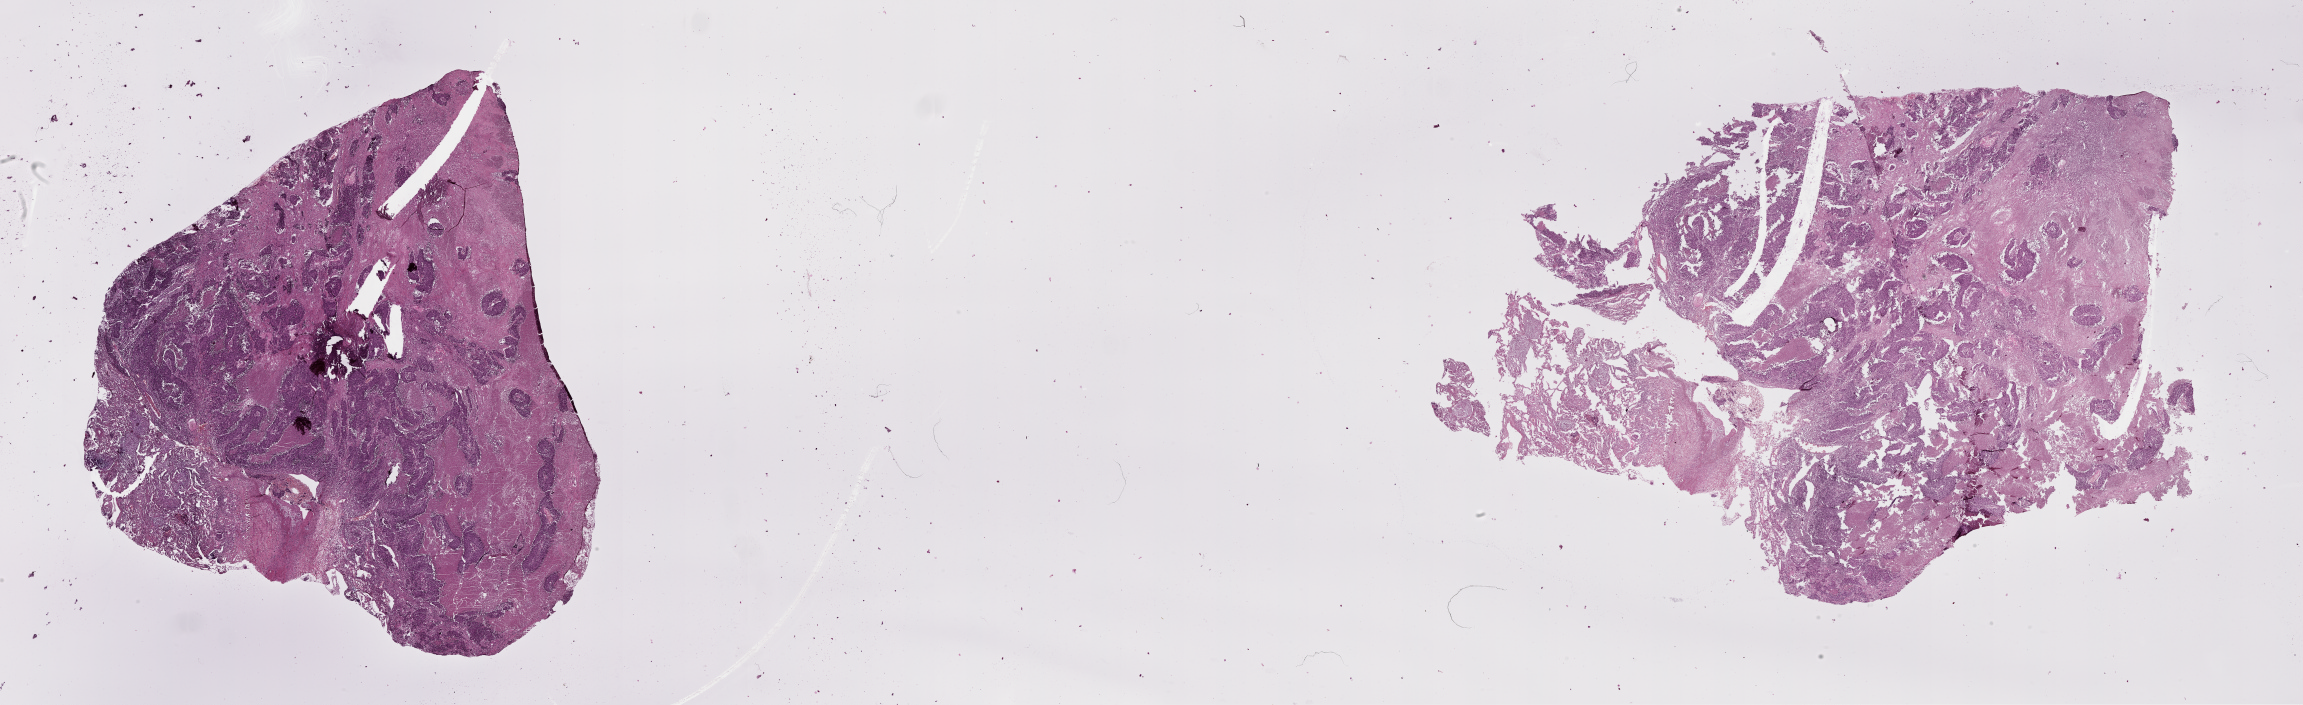
Whole-slide histology image, H&E — whole scanned area (about 37.1 x 11.4 mm, slide scanned at 20x) shown as a low-resolution overview. Tumour tissue sample, lung. 68-year-old male patient.
Patient diagnosis (cohort enrolment): squamous cell carcinoma (lung).